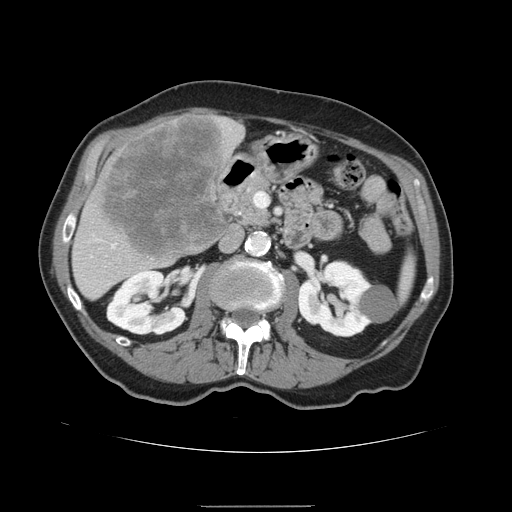
Contrast-enhanced abdominal CT, one axial slice. Slice 64 of 168 in the series (ordered by position). 120 kVp. Intravenous contrast given. Soft-tissue window (W 400 / L 40 HU). 512 × 512 image matrix, field of view 386 × 386 mm. Male patient, age 74 years. From the clinical record (not read from this slice): diagnosis: colorectal cancer liver metastases, imaged before liver resection; multiple liver metastases: no.
Outlined on this slice (manually delineated by an expert):
- liver: bounding box [x1, y1, x2, y2] px = [72, 114, 245, 300]
- planned liver remnant (the part of the liver to remain after resection): [86, 292, 97, 297]
- liver metastasis: [102, 118, 230, 258]